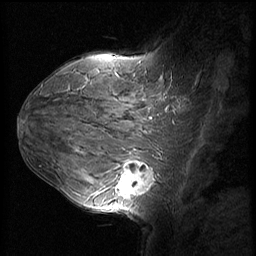
Breast MRI (dynamic contrast-enhanced), one sagittal slice; slice 39 of 60 in the series (ordered by position); dynamic contrast-enhanced series, image 2 of 3 at this slice position (ordered by acquisition); 1.5 T; TE 4.2 ms, TR 8.9 ms; 256 × 256 image matrix. Female patient, age 37 years. Case-level facts recorded for this patient, not image findings: setting: breast cancer imaged before/during neoadjuvant chemotherapy; receptor status: triple-negative.
Annotated regions visible in this slice (semi-automatic segmentation, software-assisted and operator-edited):
- analysis volume of interest (the breast-tissue region the enhancement analysis was run in; not a lesion): bounding box (x1, y1, x2, y2) in pixels: (114, 153, 159, 206)
- tumour enhancement mask (voxels above the 140 % enhancement threshold inside the analysis volume of interest): (118, 162, 155, 199)